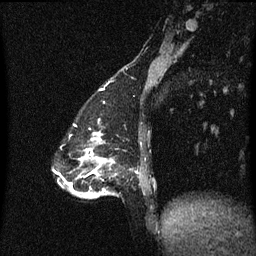
Breast MRI (dynamic contrast-enhanced), one sagittal slice; slice 15 of 60 in the series (ordered by position); dynamic contrast-enhanced series, image 2 of 3 at this slice position (ordered by acquisition); 1.5 T; TE 4.2 ms, TR 8.4 ms; 256 × 256 image matrix. Patient: female, 47 years.
Annotated regions visible in this slice (semi-automatic segmentation, software-assisted and operator-edited):
- analysis volume of interest (the breast-tissue region the enhancement analysis was run in; not a lesion): bounding box (x1, y1, x2, y2) in pixels: (81, 138, 116, 199)
- tumour enhancement mask (voxels above the 70 % enhancement threshold inside the analysis volume of interest): (88, 138, 105, 193)